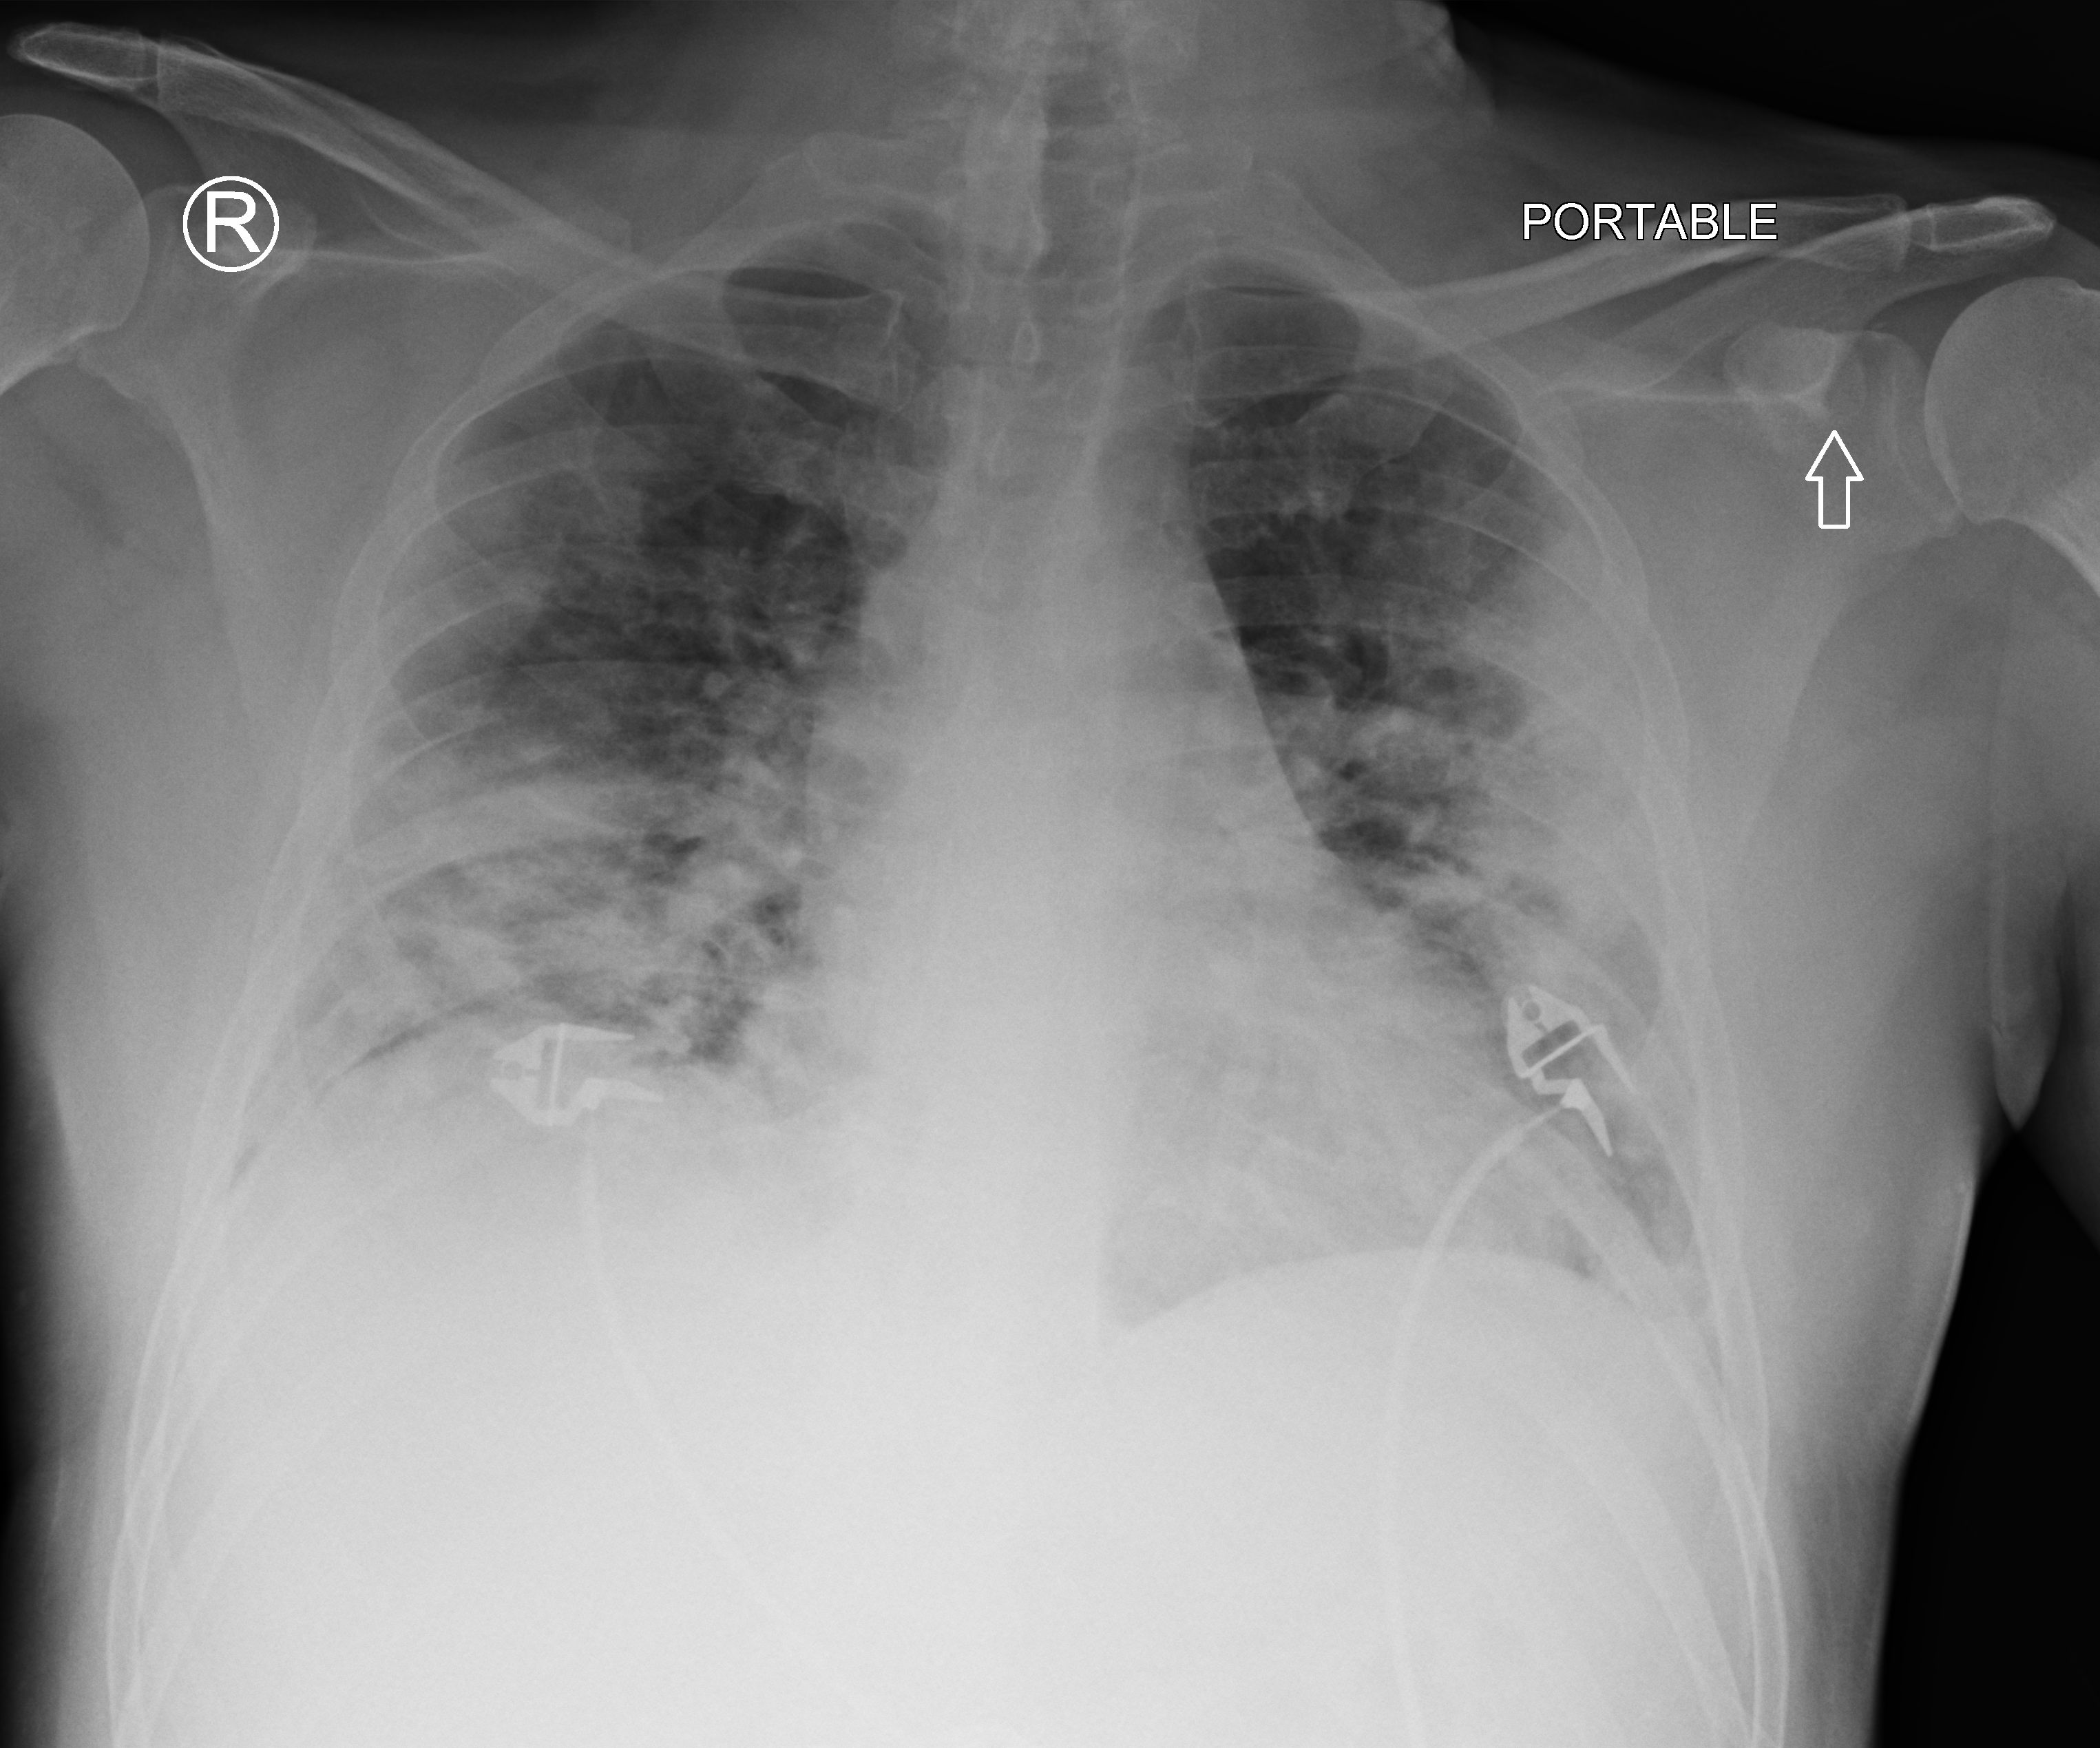
Portable chest radiograph. Male patient hospitalised with COVID-19, age 18–59 years.
Hospital-stay facts (about this admission, not read from this image; timing relative to this image not recorded): mechanically ventilated during this hospital stay: no; admitted to intensive care during this hospital stay: no.